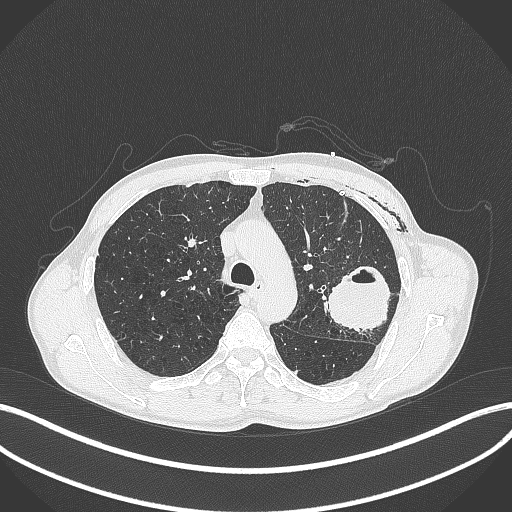
Chest CT, one axial slice. Position 286 of 457 along the scan axis. Reconstruction kernel B70f. 120 kVp. Lung window (W 1500 / L -600 HU). 1 mm slice thickness. 512 × 512 image matrix, field of view 400 × 400 mm. Patient: male, 58 years. From the clinical record (not read from this slice): clinical TNM (as recorded): T3 N0 M0.
Structures marked on this image (bounding box drawn by a radiologist):
- lung tumour (recorded histology: adenocarcinoma): bounding box (x1, y1, x2, y2) in pixels: (323, 265, 394, 336)